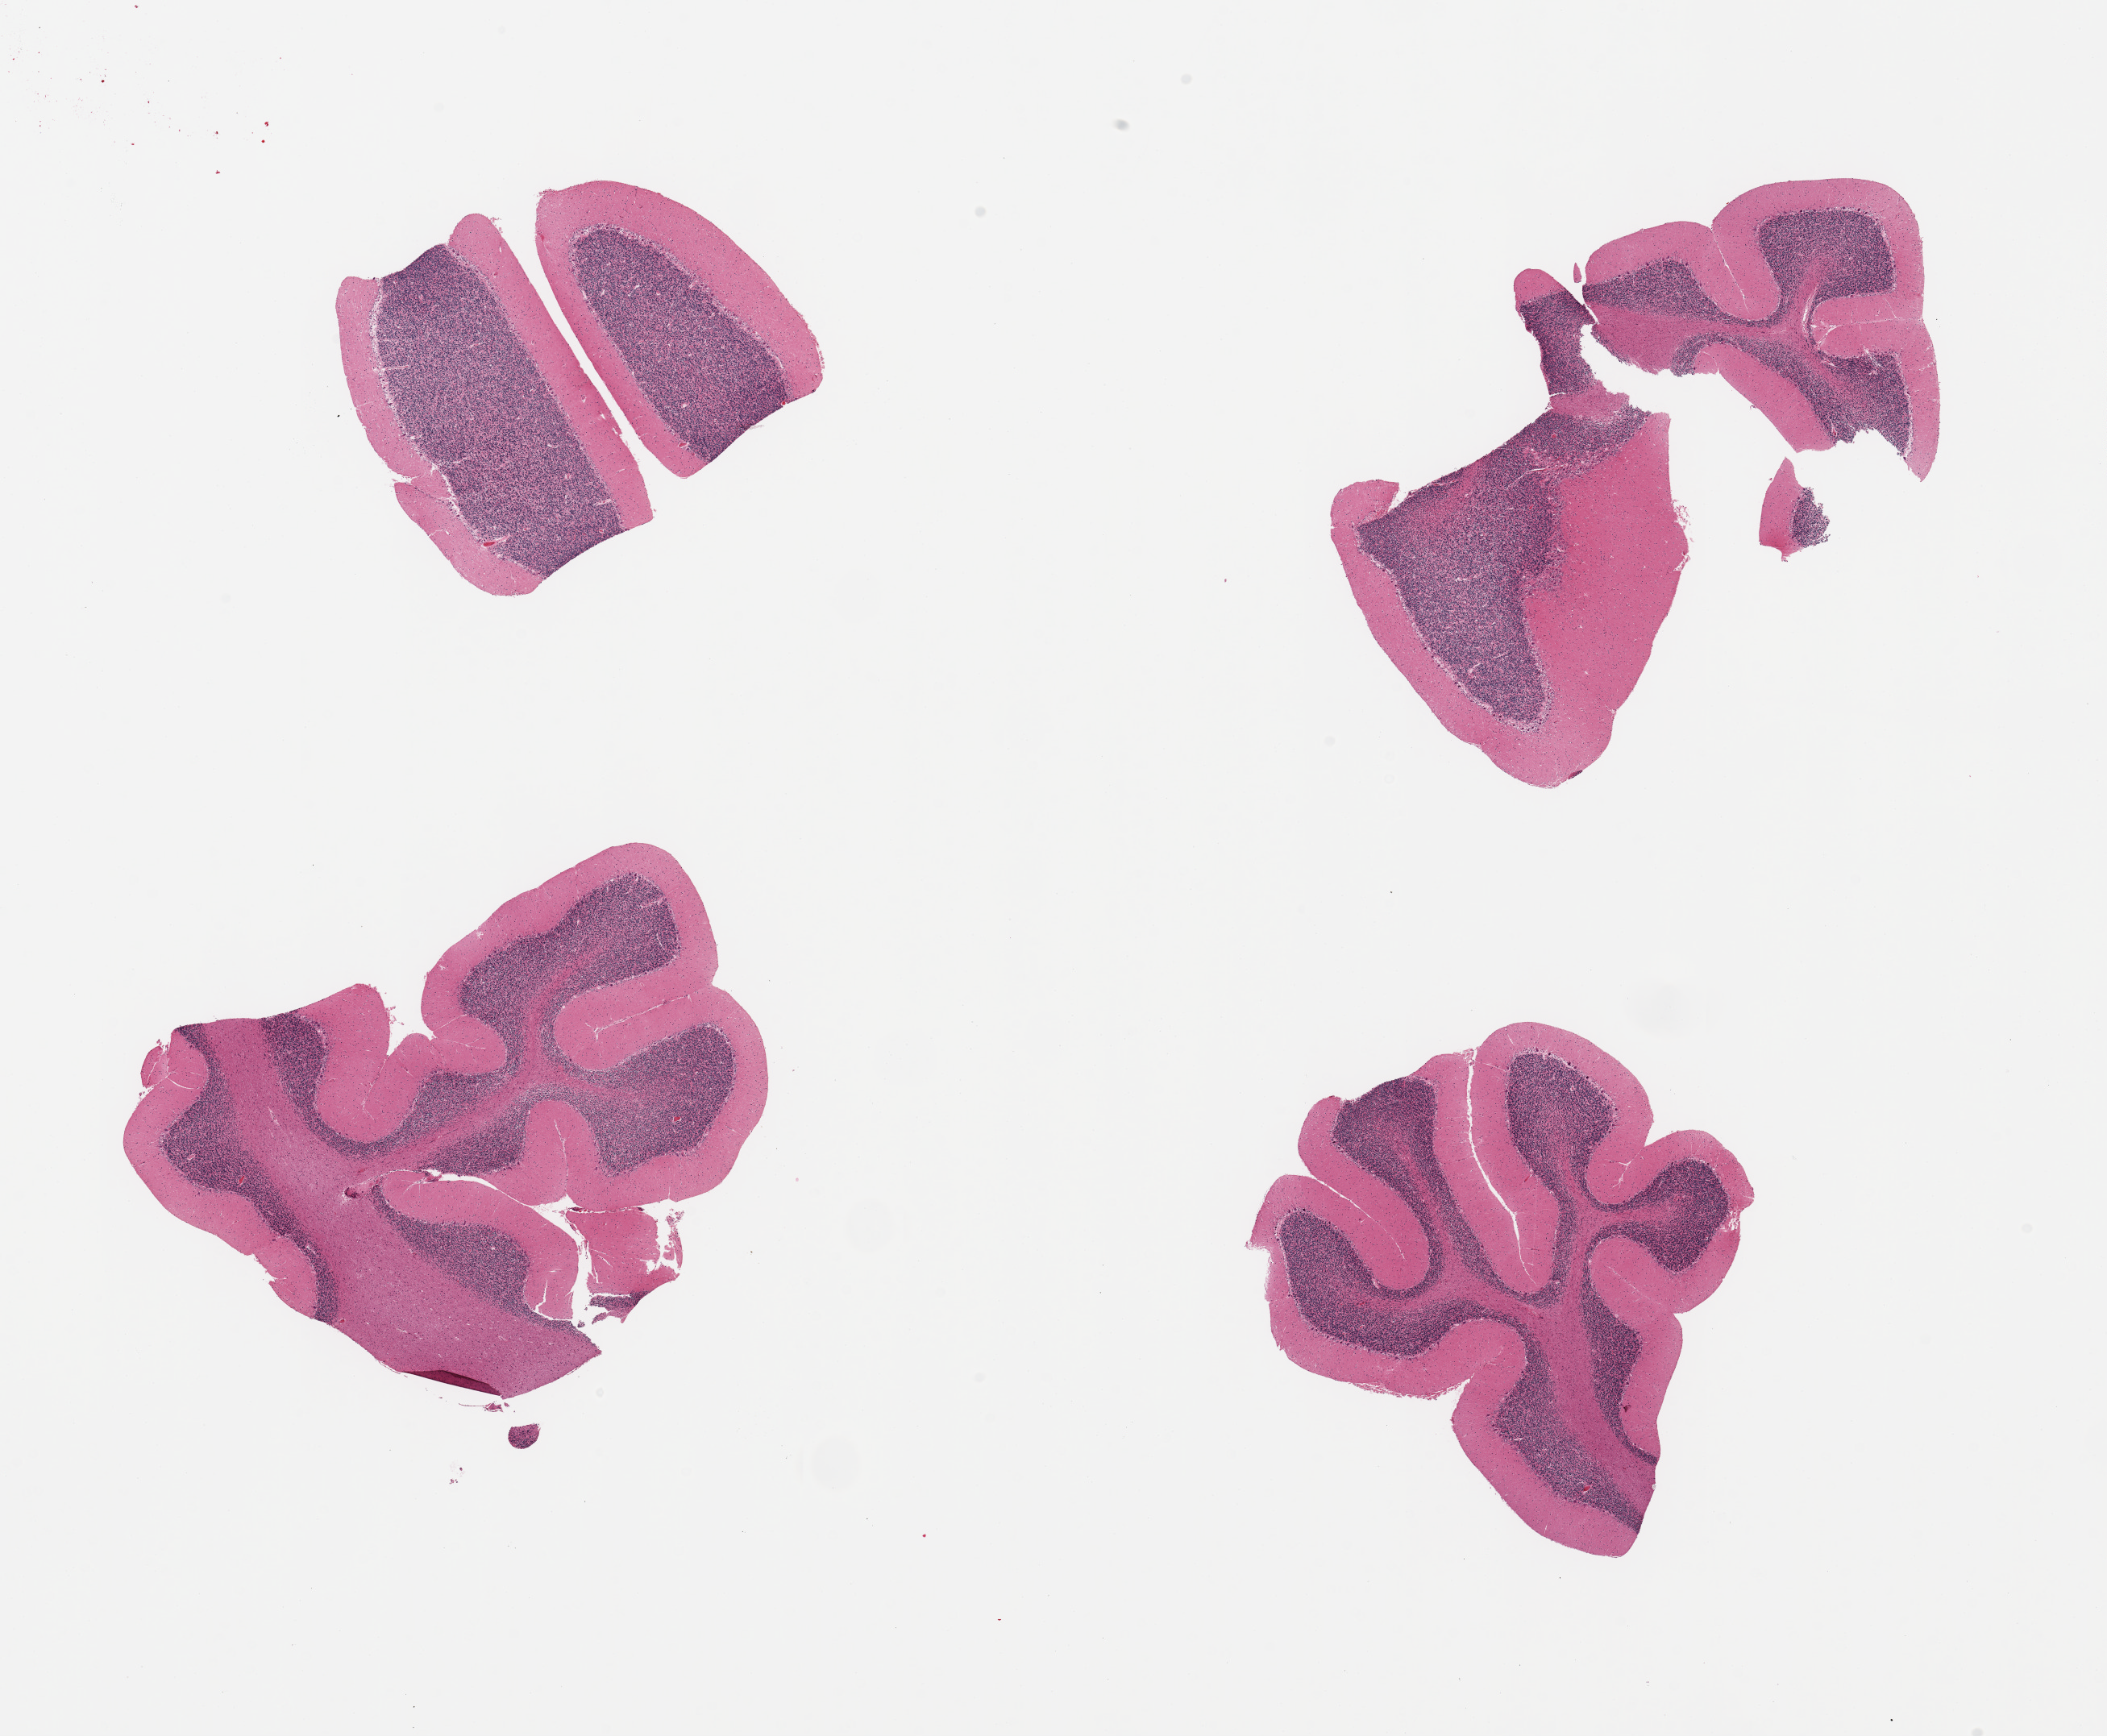
Whole-slide image, haematoxylin and eosin stain, low-resolution overview of the scanned area, about 20.7 x 17.0 mm (slide scanned at 20x), PAXgene-fixed, paraffin-embedded tissue, section of cerebellum (target tissue), donor tissue sample. Donor: female.
Pathologist's review note for this sample: 4 pieces.